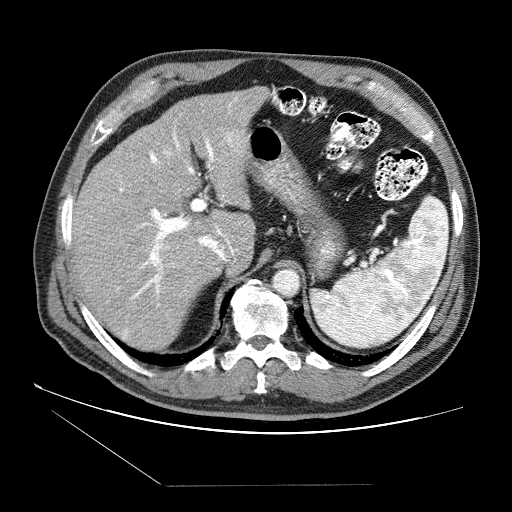
Contrast-enhanced abdominal CT (liver protocol), one axial slice; position 55 of 87 along the scan axis; soft-tissue window (W 400 / L 40 HU); 2.5 mm slice thickness; 512 × 512 image matrix. From the clinical record (not read from this slice): diagnosis: hepatocellular carcinoma (patient treated with transarterial chemoembolisation; whether this scan precedes or follows treatment is not stated here); TNM stage (as recorded): Stage-II; Child-Pugh class: B; tumour nodularity: multinodular.
Structures marked on this image (semi-automatic segmentation, software-assisted and operator-edited):
- liver parenchyma outside the tumour (the mass and vessels are separate outlines, so this box may not span the whole liver): bounding box (x1, y1, x2, y2) in pixels: (70, 86, 268, 348)
- liver vessels: (71, 98, 250, 339)